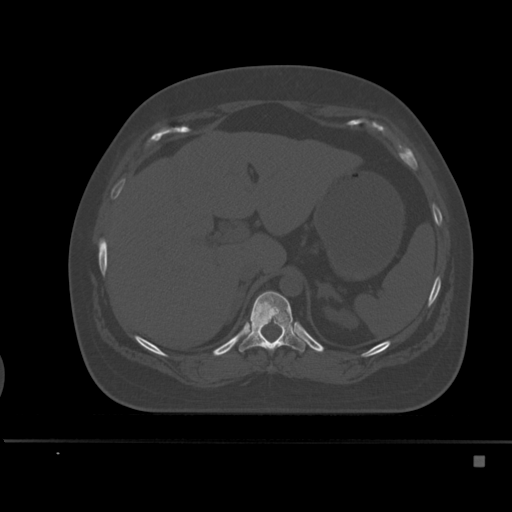
CT including the spine, one axial slice. Bone window (W 1800 / L 400 HU). 512 × 512 image matrix, field of view 404 × 404 mm. Patient: female, 33 years. Case-level facts recorded for this patient, not image findings: primary cancer: breast; vertebrae with lytic lesions (as recorded): T1.
Structures marked on this image (semi-automatic segmentation, software-assisted and operator-edited):
- T11 vertebra: box from (x=239, y=291) to (x=308, y=352) px